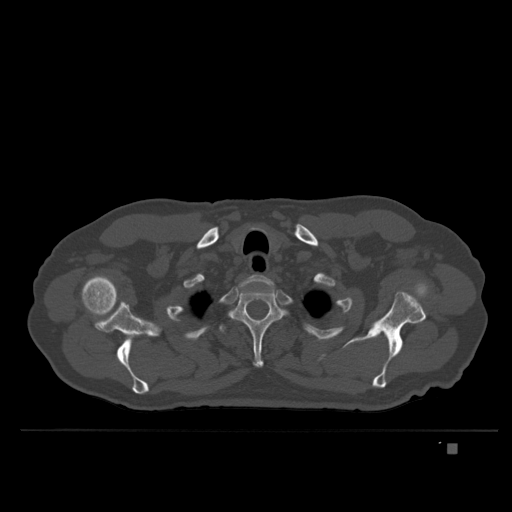
CT including the spine, one axial slice; position 313 of 435 along the scan axis; bone window (W 1800 / L 400 HU); 1.5 mm slice thickness; 512 × 512 image matrix, field of view 434 × 434 mm. Male patient, age 73 years. From the clinical record (not read from this slice): primary cancer: skin.
Outlined on this slice (semi-automatically segmented with operator editing):
- T1 vertebra: bounding box (x1, y1, x2, y2) in pixels: (242, 274, 273, 286)
- T2 vertebra: (229, 288, 285, 367)
- T3 vertebra: (219, 324, 226, 334)